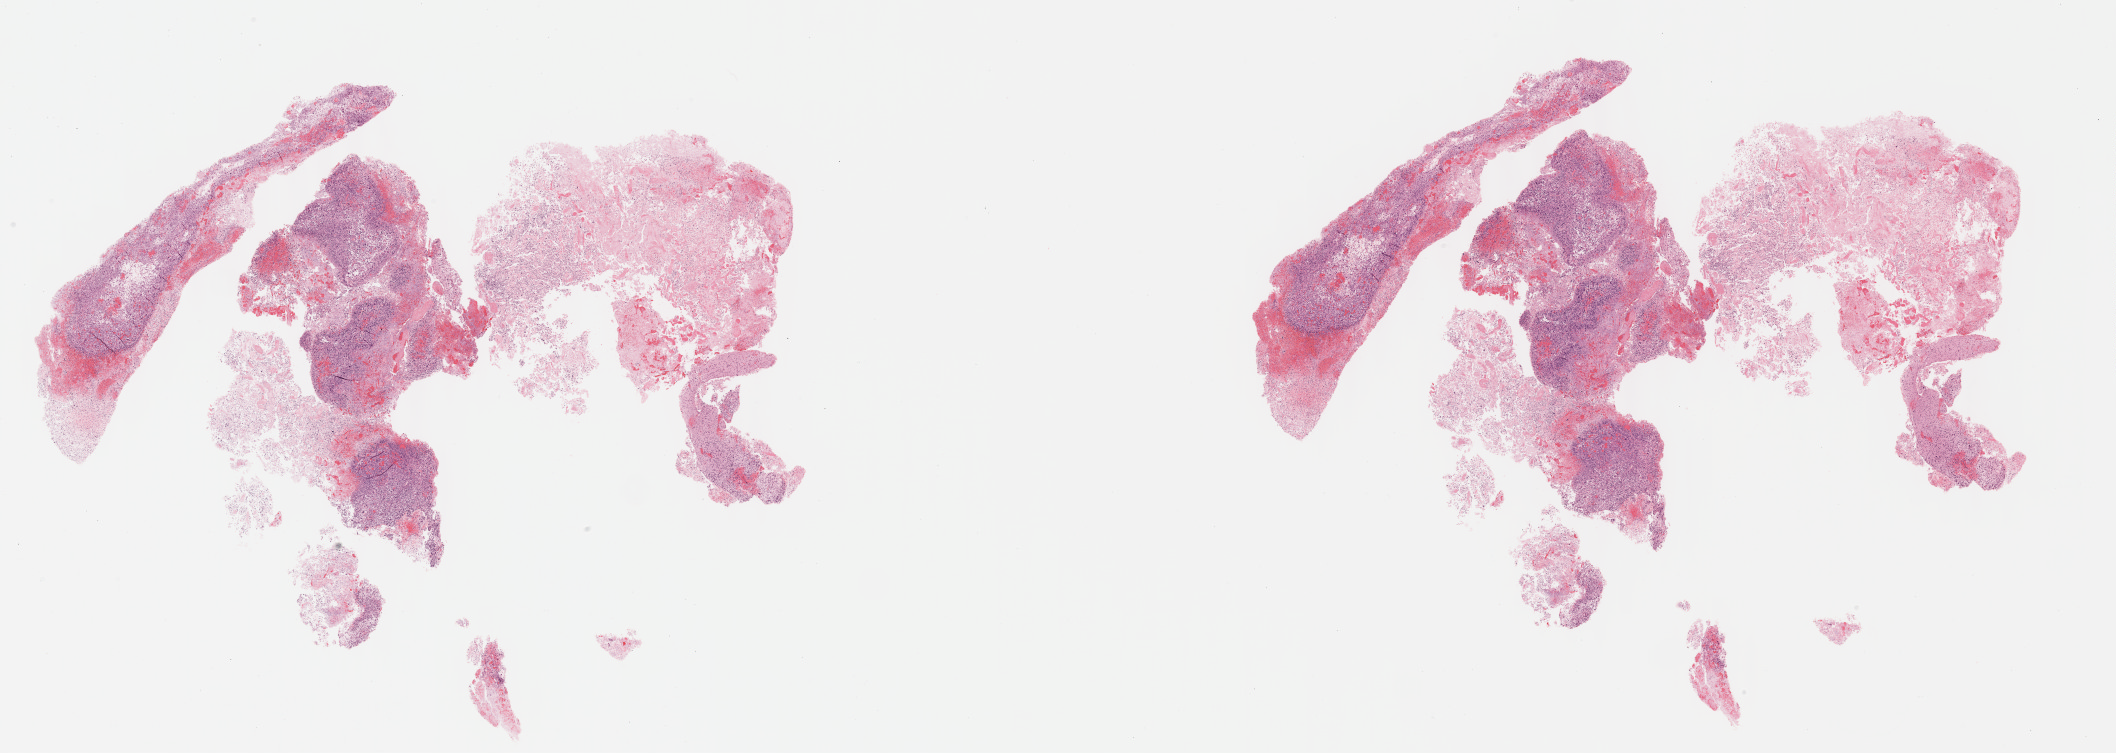
Whole-slide histology image, H&E-stained, low-resolution overview of the scanned area, about 34.2 x 12.2 mm (slide scanned at 40x), formalin-fixed paraffin-embedded (FFPE) diagnostic section, brain, primary tumour sample. Patient: male, age at initial diagnosis 46 years.
* histologic diagnosis: Glioblastoma